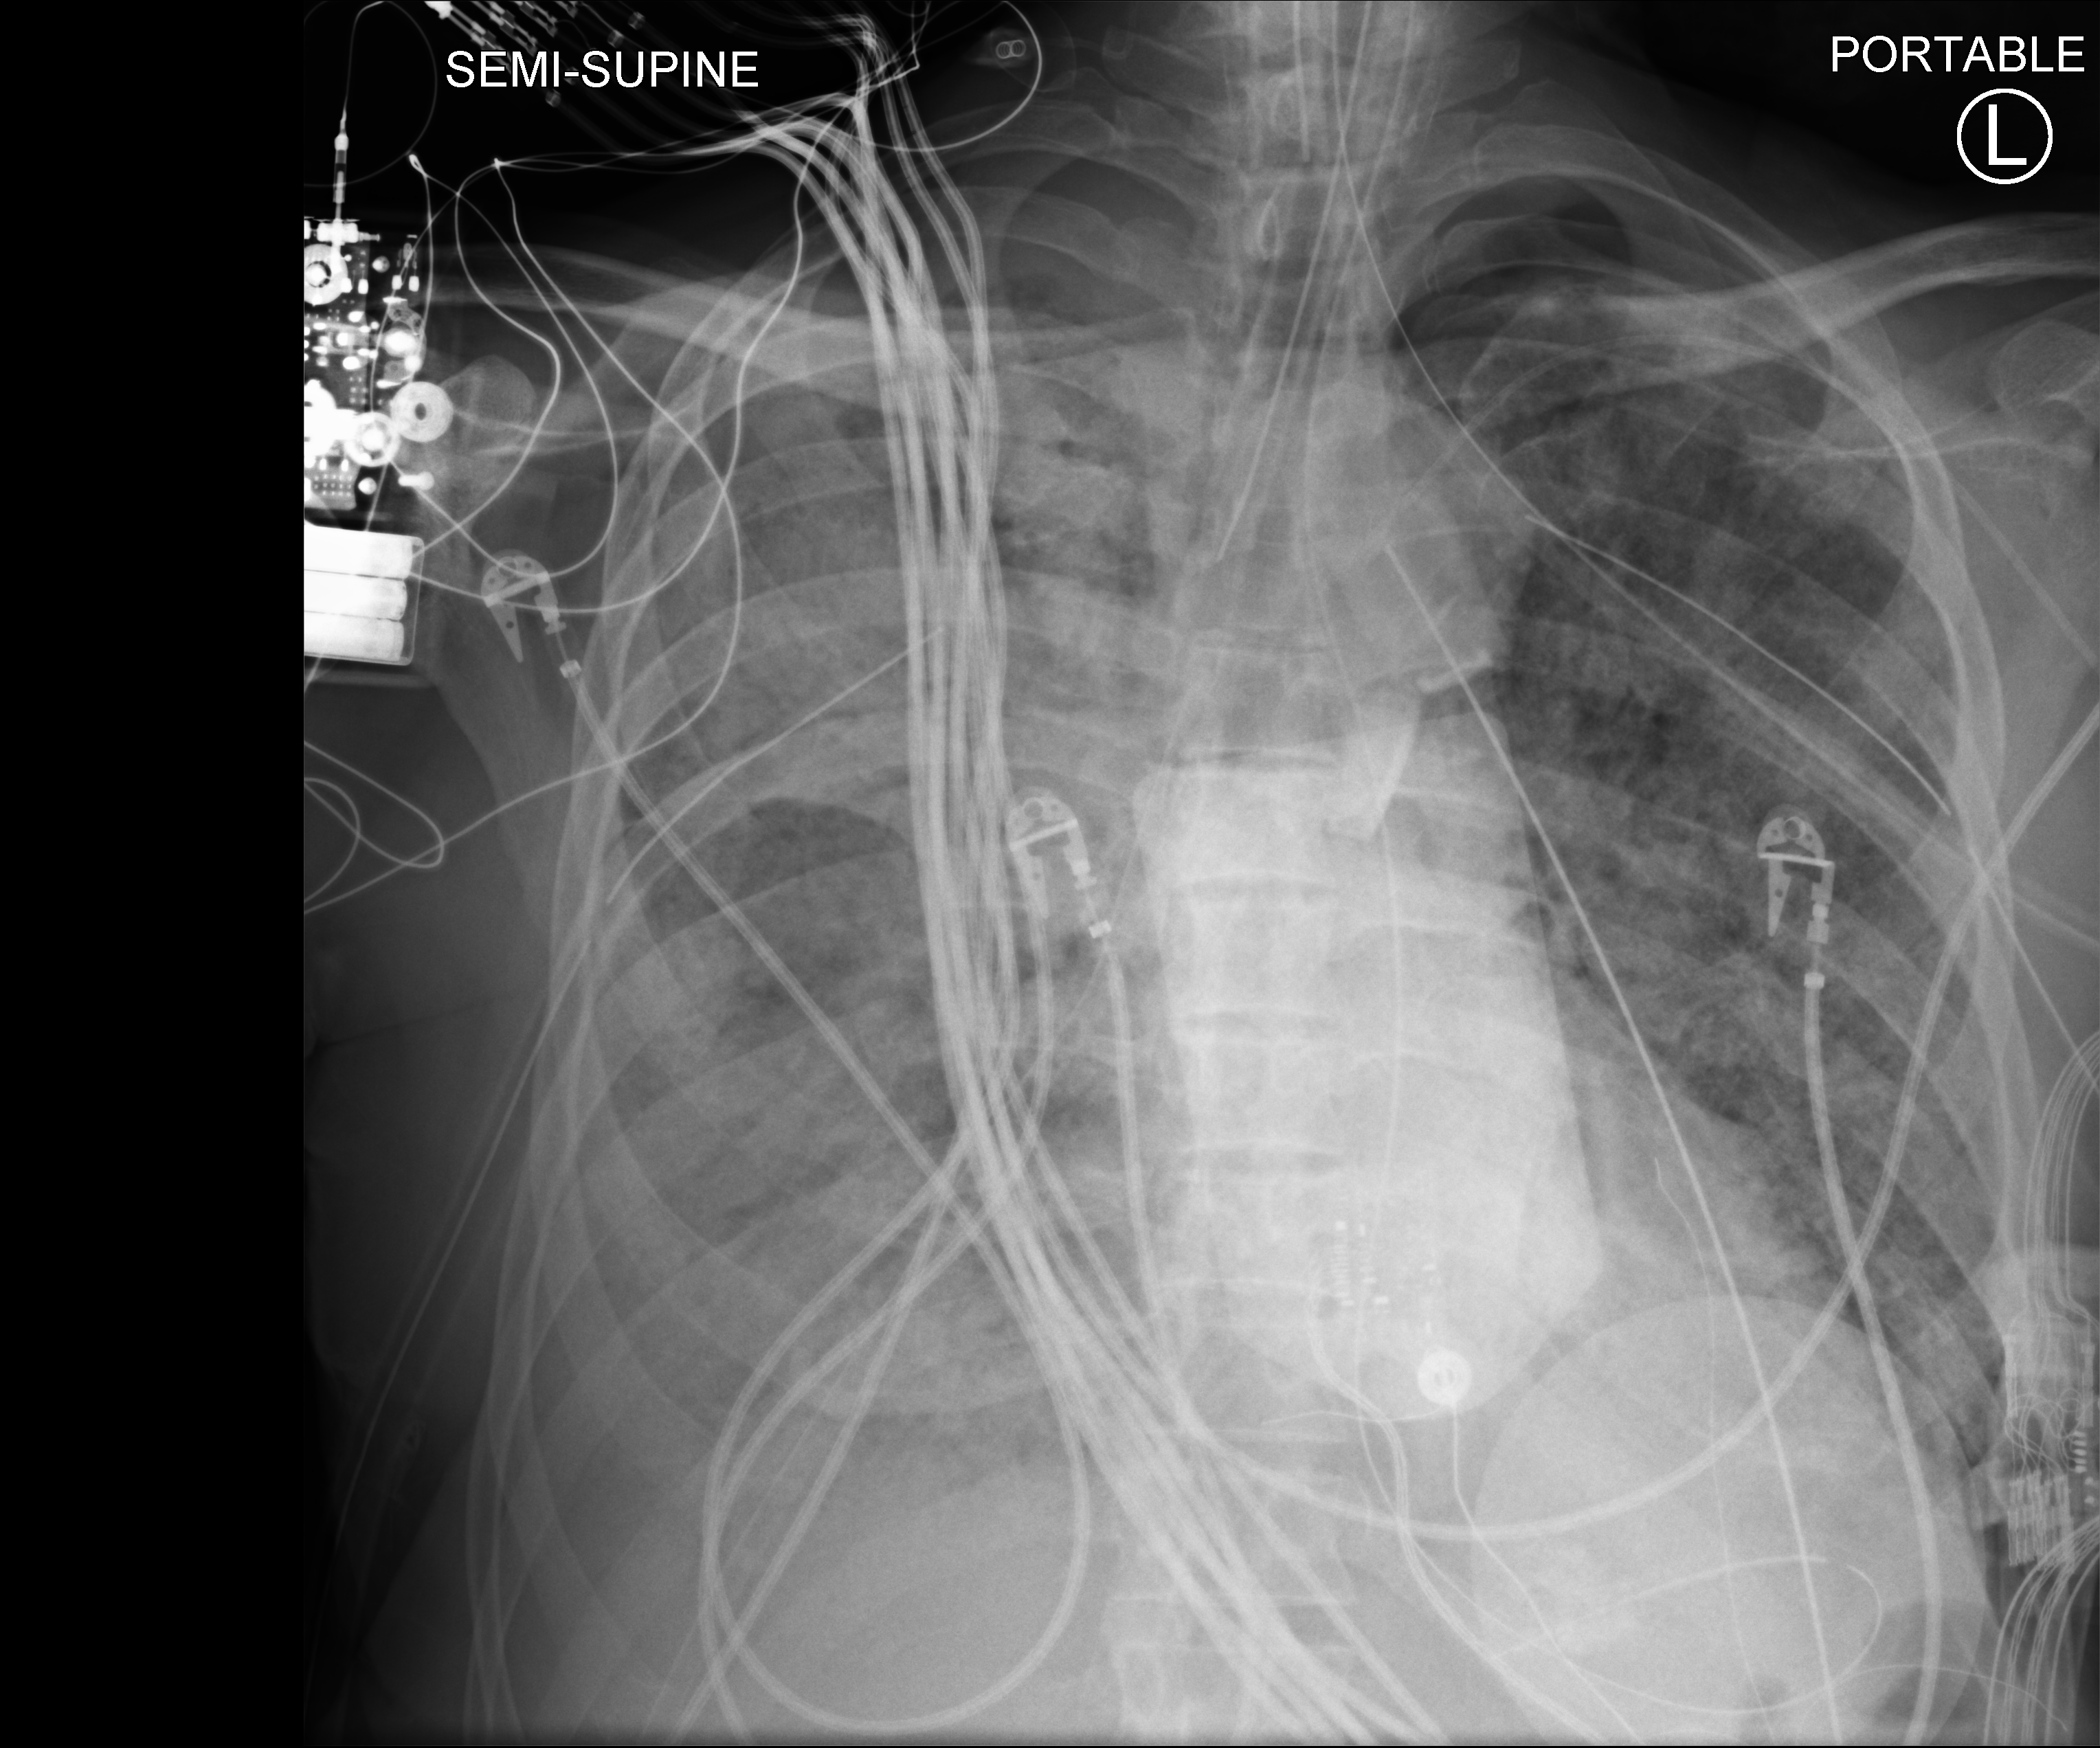
Bedside chest radiograph (computed radiography), anteroposterior (AP) projection. Male patient hospitalised with COVID-19, age 60–74 years.
Hospital-stay facts (about this admission, not read from this image; timing relative to this image not recorded):
- COPD (admission record): no
- admitted to intensive care during this hospital stay: yes
- length of hospital stay: 31 days